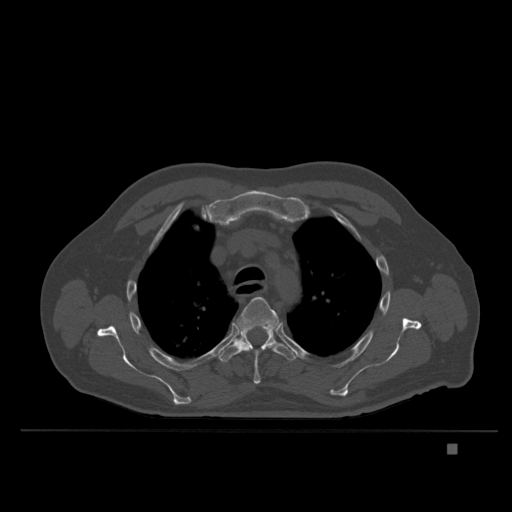
CT including the spine, one axial slice. Slice 281 of 435 in the series (ordered by position). Bone window (W 1800 / L 400 HU). 512 × 512 image matrix, field of view 434 × 434 mm. Male patient, age 73 years. From the clinical record (not read from this slice): primary cancer: skin.
Outlined on this slice (semi-automatic segmentation, software-assisted and operator-edited):
- T4 vertebra: box from (x=233, y=297) to (x=279, y=384) px
- T5 vertebra: (x=220, y=329)–(x=295, y=363)